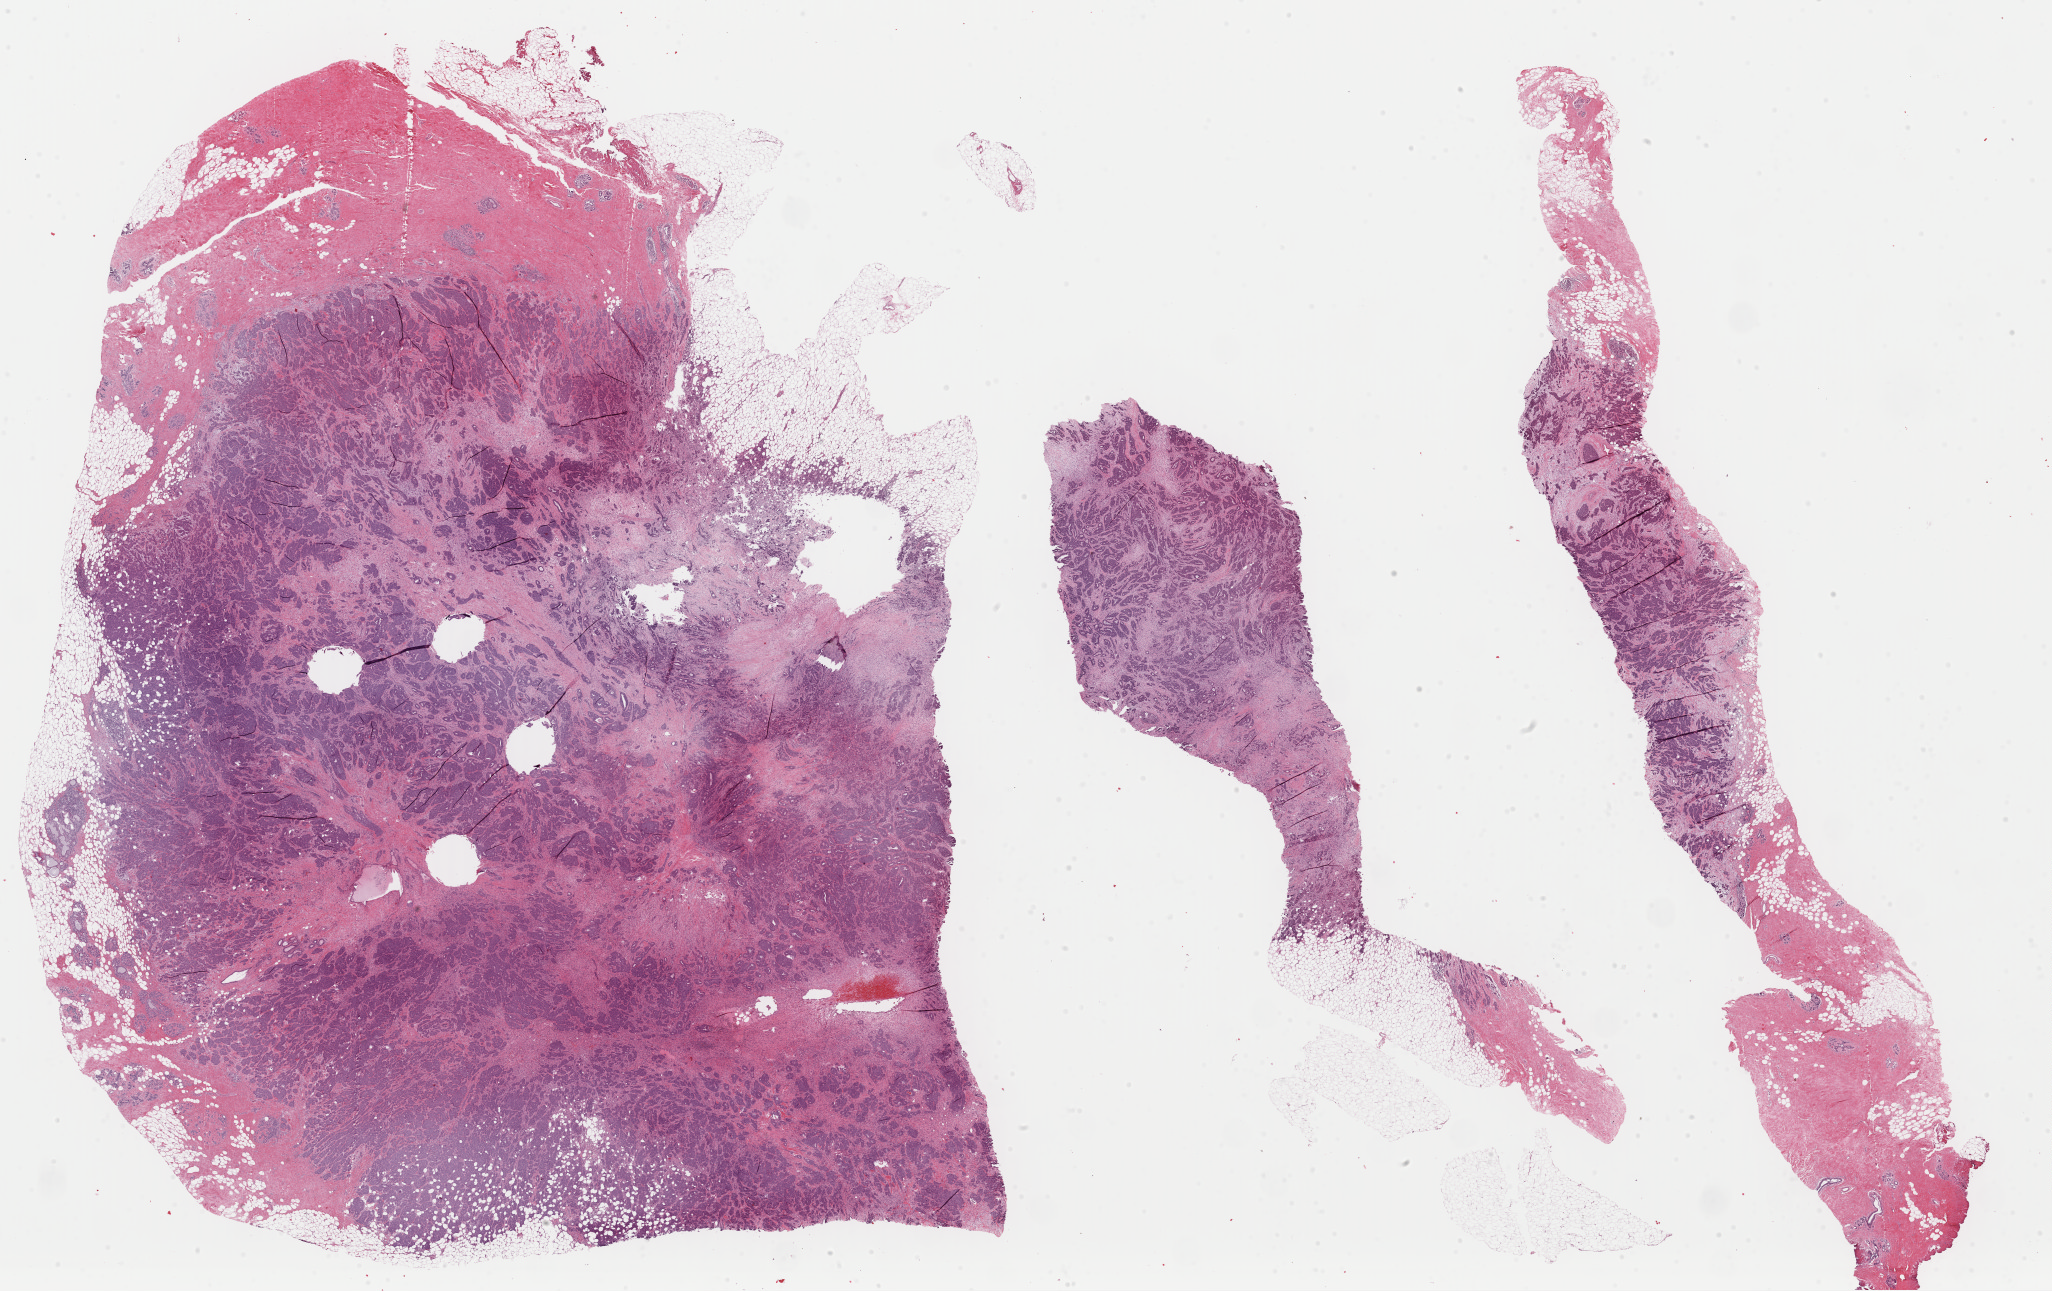
Digitized Hematoxylin and eosin (H&E) stained tissue section (whole slide) — shown as a low-resolution overview of the whole scanned area (about 32.4 x 20.4 mm, acquisition: 40x scan); formalin-fixed paraffin-embedded (FFPE) diagnostic section; sample: primary tumour, breast. Patient: female, age at initial diagnosis 46 years.
Lymph nodes positive (case pathology): 0 of 2 examined. Laterality: left. AJCC pathologic stage: IIA (6th edition). Histologic diagnosis: Infiltrating duct carcinoma, NOS.